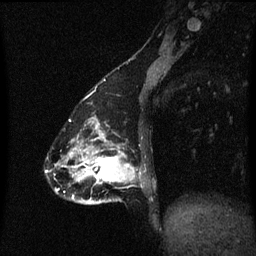
Breast MRI (dynamic contrast-enhanced), one sagittal slice; dynamic contrast-enhanced series, image 2 of 3 at this slice position (ordered by acquisition); 1.5 T; TE 4.2 ms, TR 8.4 ms; 2 mm slice thickness; 256 × 256 image matrix. Patient: female, 47 years.
Structures marked on this image (semi-automatic segmentation, software-assisted and operator-edited):
- analysis volume of interest (the breast-tissue region the enhancement analysis was run in; not a lesion): bounding box [x1, y1, x2, y2] px = [81, 138, 145, 205]
- tumour enhancement mask (voxels above the 70 % enhancement threshold inside the analysis volume of interest): [82, 138, 141, 185]